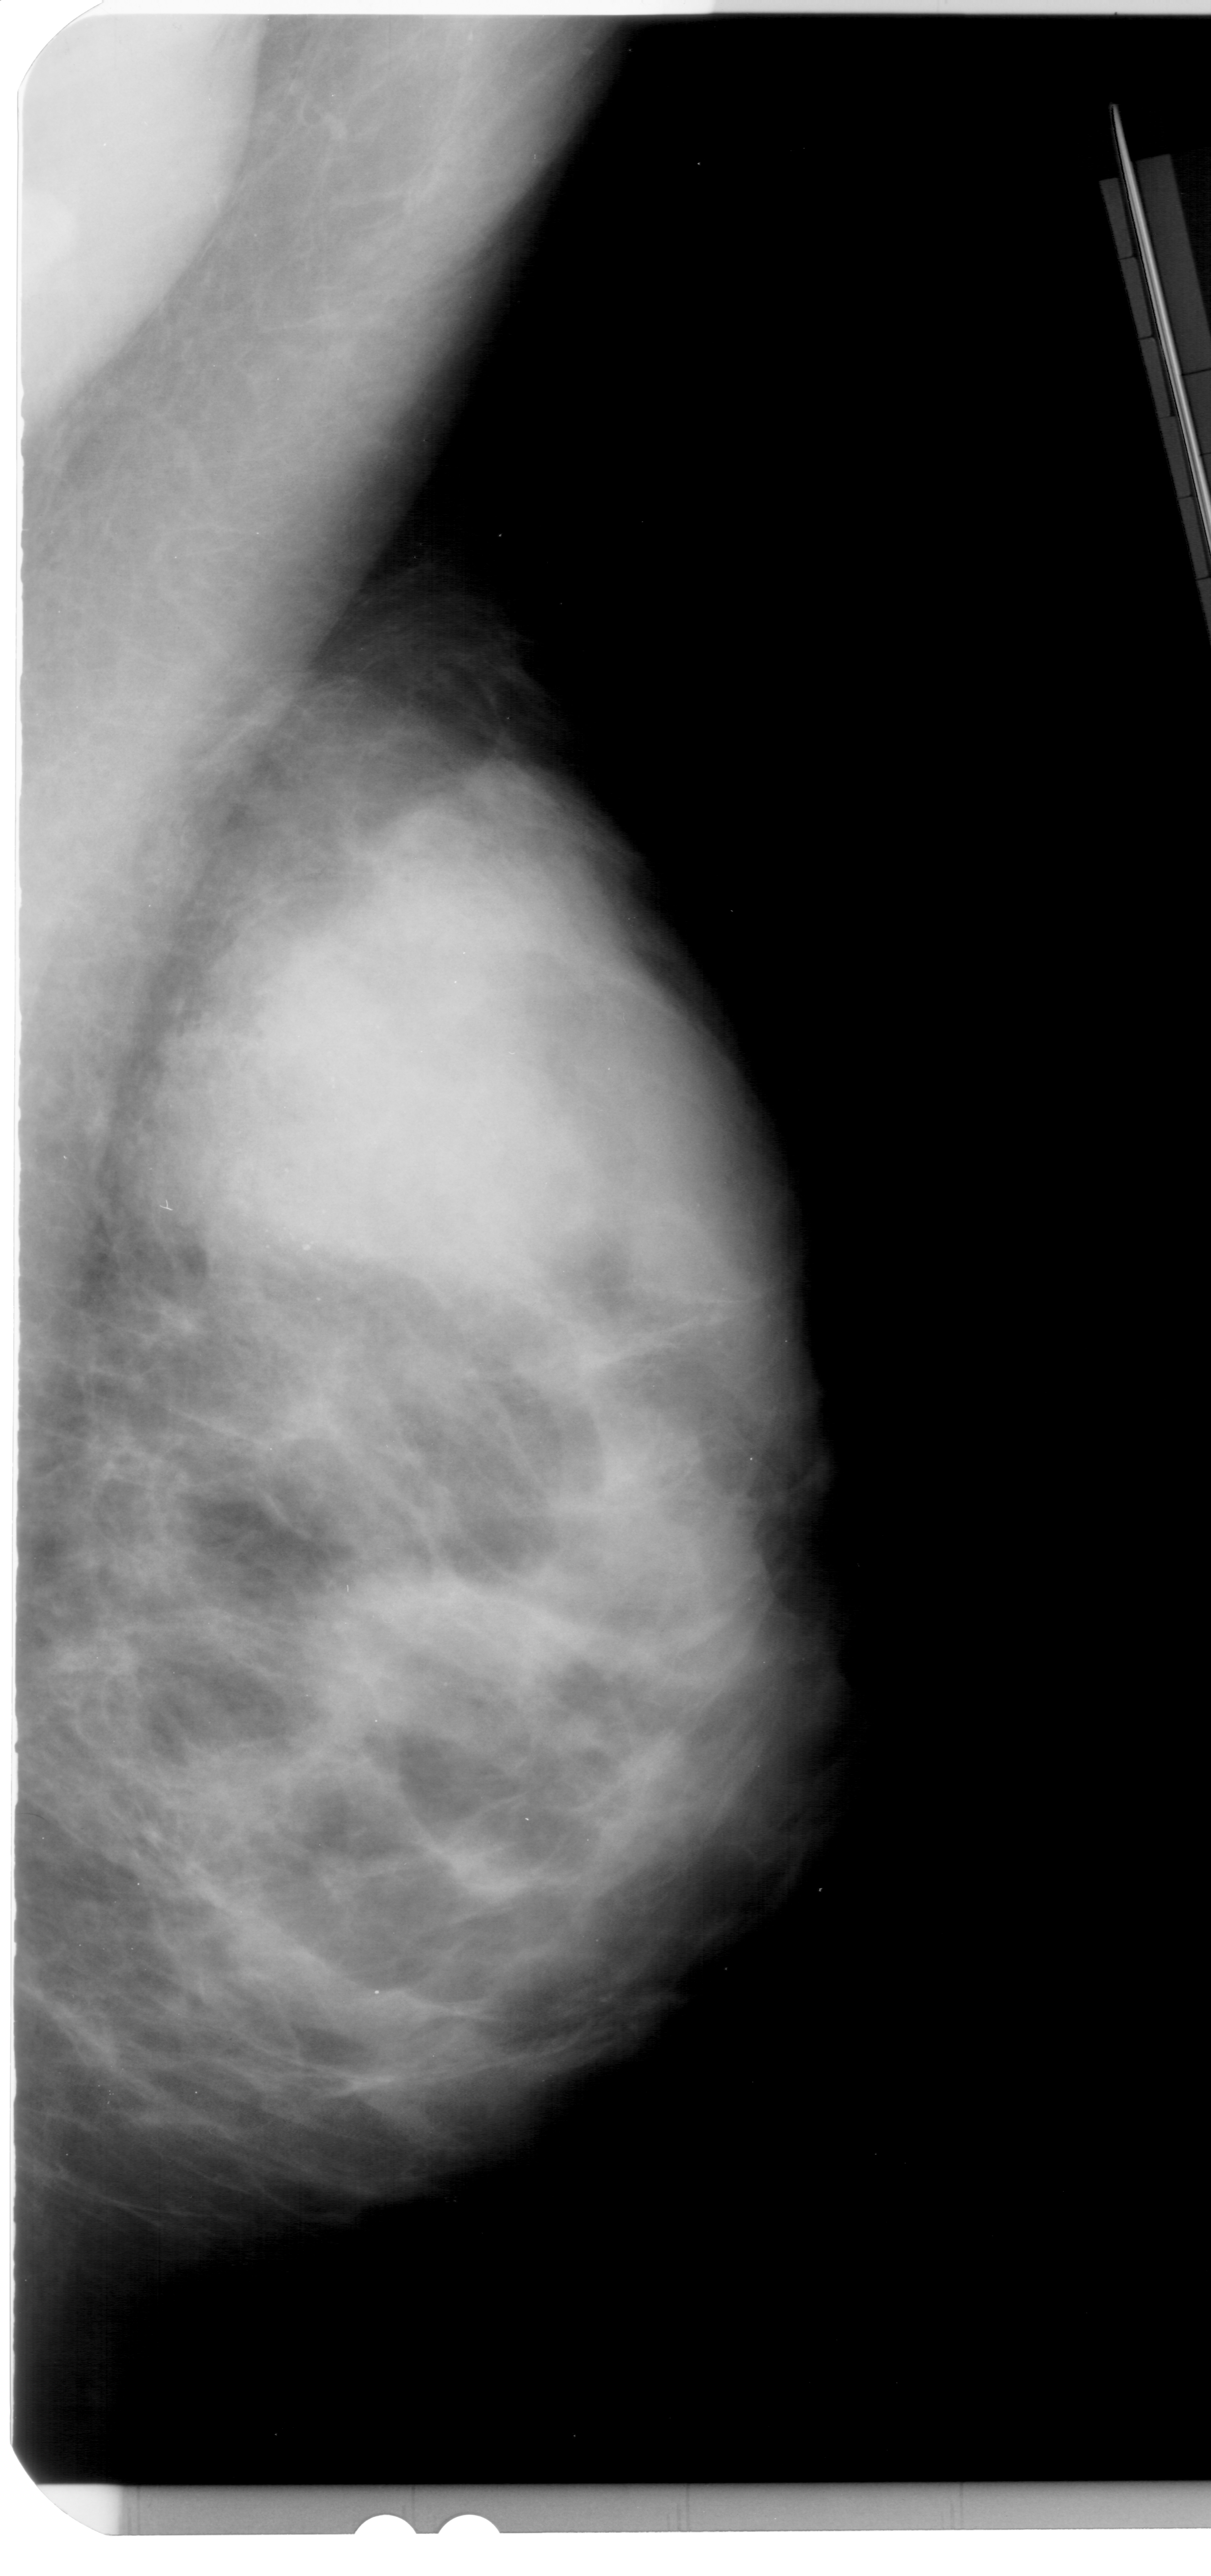
Digitized screen-film mammogram; right breast; mediolateral oblique (MLO) view; breast composition: extremely dense (BI-RADS density category 4 of 4).
Marked abnormality: calcifications, morphology amorphous, distribution segmental; BI-RADS assessment category 4; pathology (as recorded): benign.